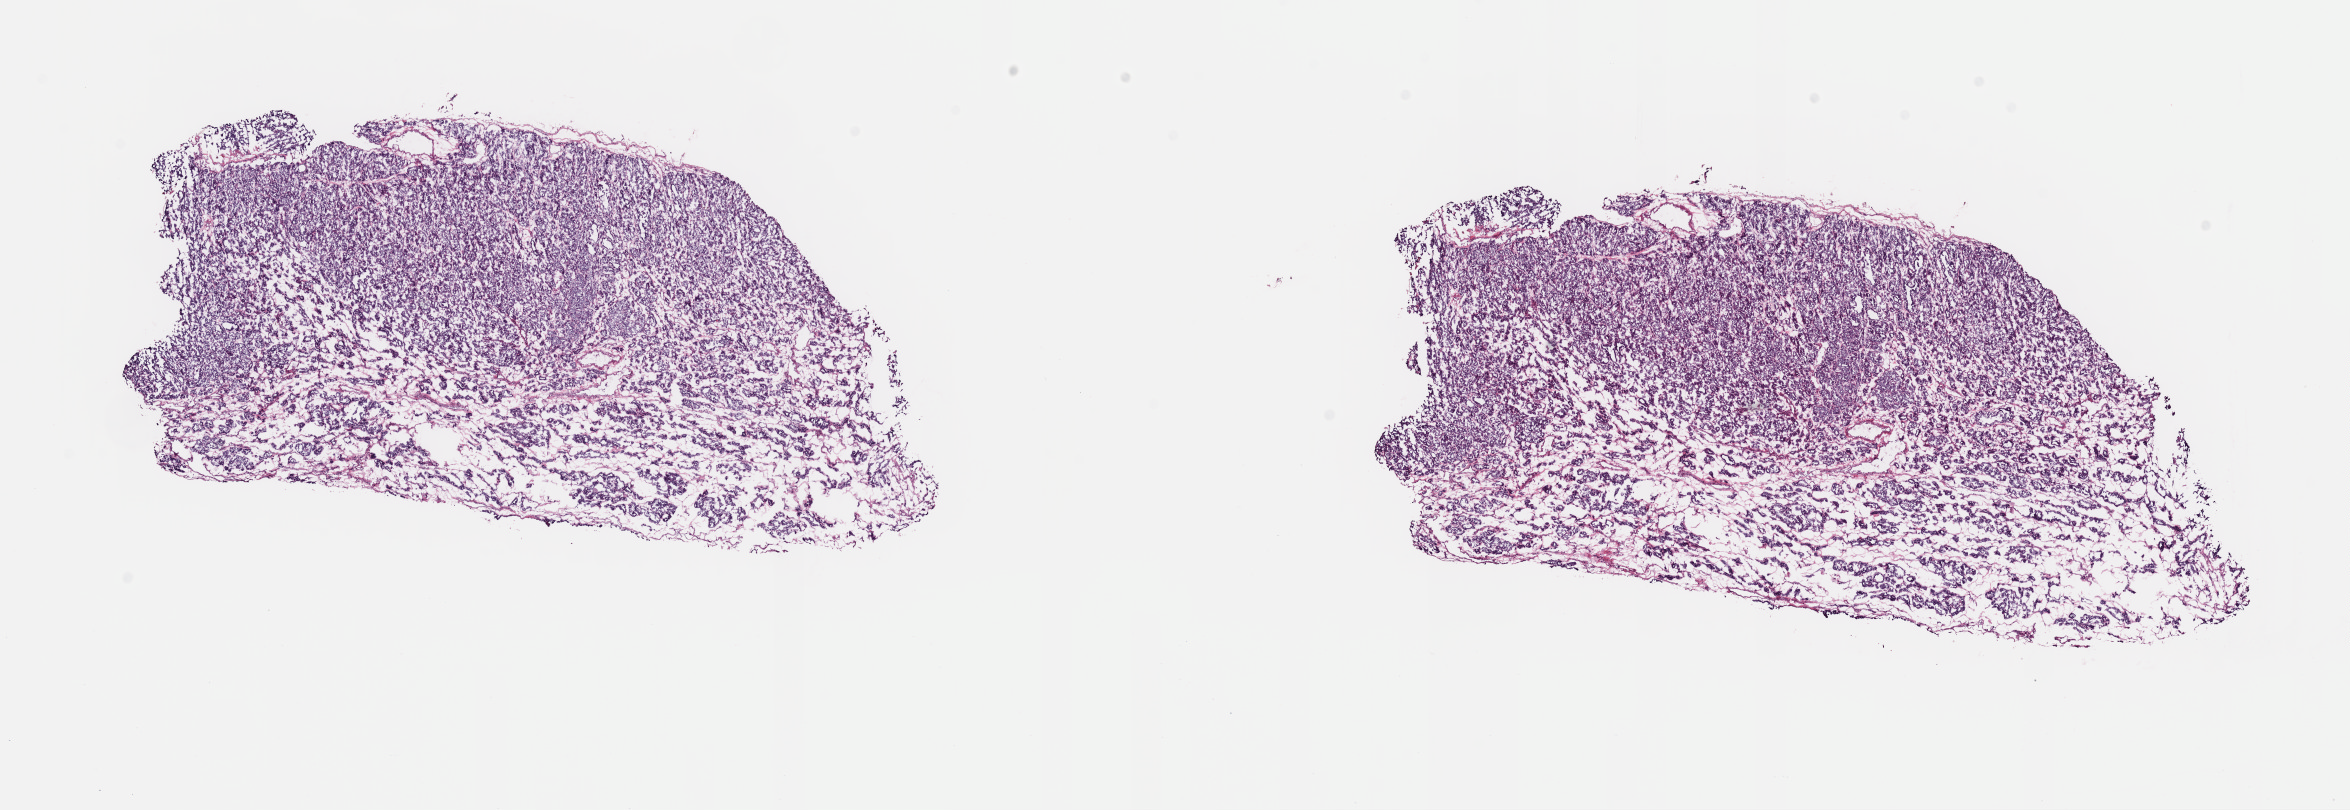
Digitized H&E tissue section (whole slide) — shown as a low-resolution overview of the whole scanned area (about 18.6 x 6.4 mm), frozen section, sample: primary tumour, thyroid. Female, age 67 years at initial diagnosis. Pathologist review of this section (percent, as recorded): tumour cells 90%, tumour nuclei 95%, normal cells 0%, stromal cells 10%, necrosis 0%. Infiltration values recorded for this section: lymphocyte infiltration 0%, monocyte infiltration 0%, neutrophil infiltration 1%.
AJCC pathologic stage: II (7th edition). Pathologic diagnosis: Papillary carcinoma, follicular variant (thyroid gland). Laterality: right.